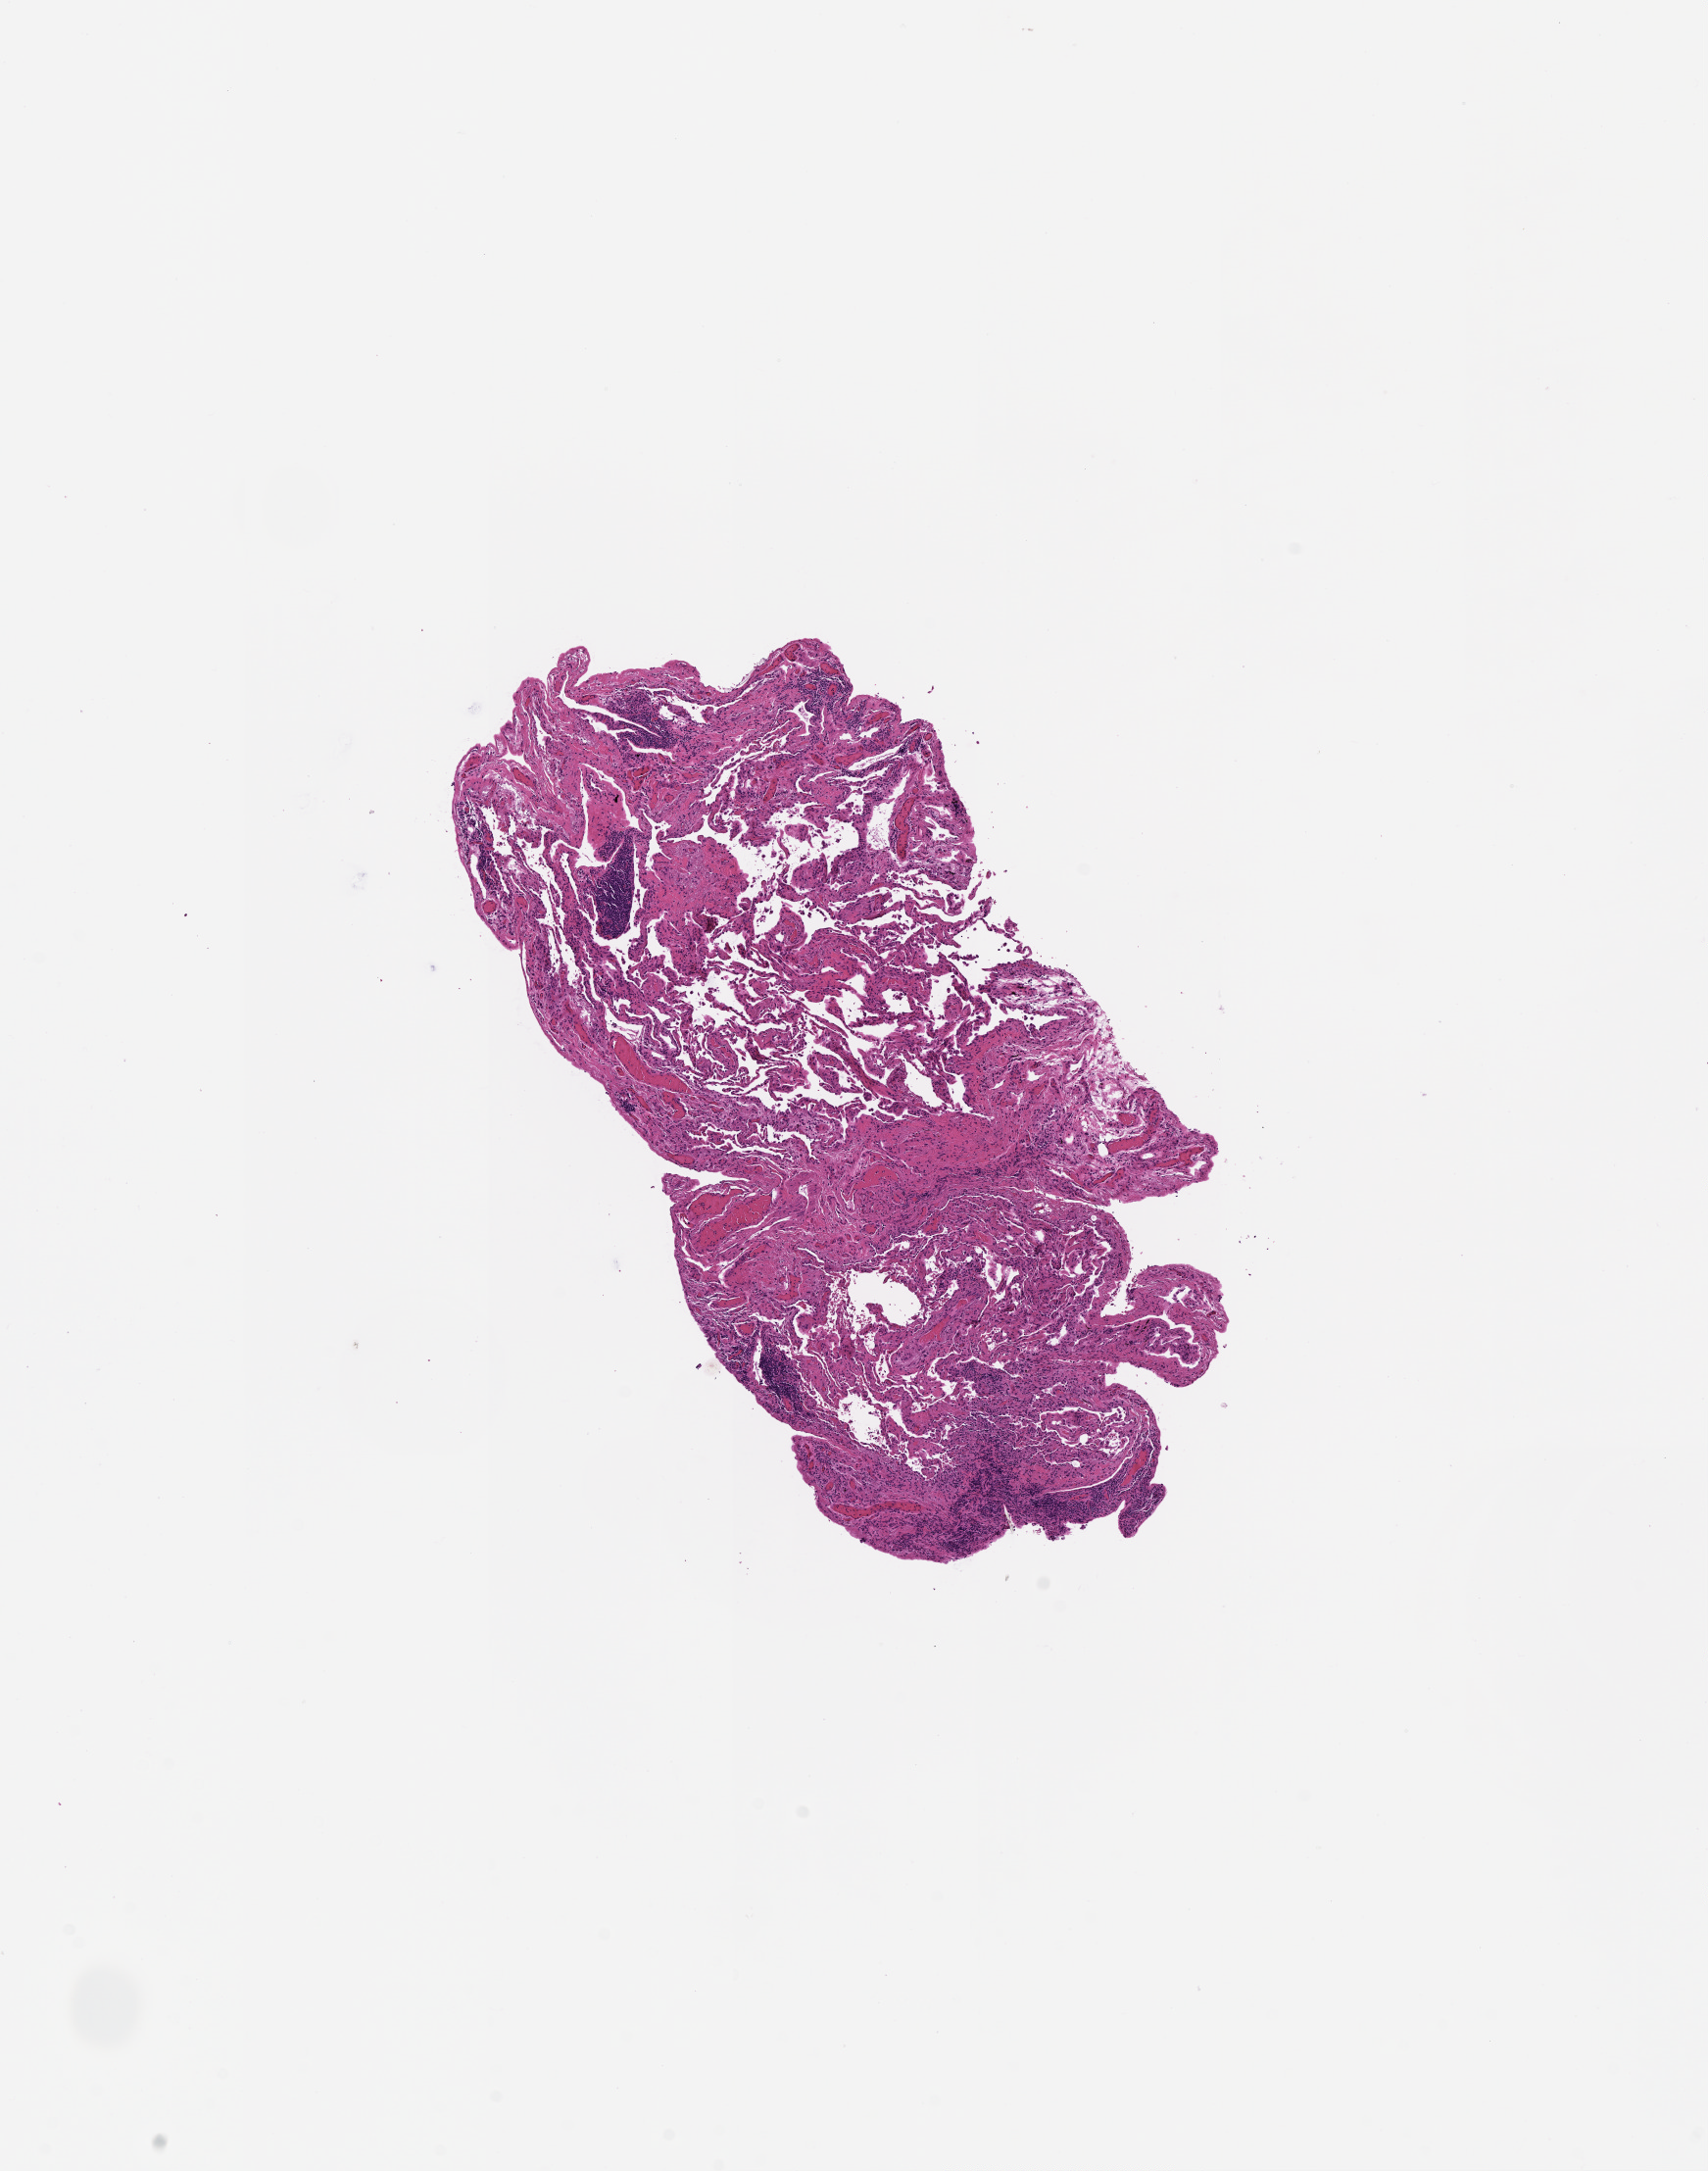
Whole-slide histology image, H&E-stained — whole scanned area (about 7.0 x 8.9 mm, slide scanned at 20x) shown as a low-resolution overview; lung, tissue type not recorded.
Patient diagnosis (cohort enrolment): squamous cell carcinoma (lung).